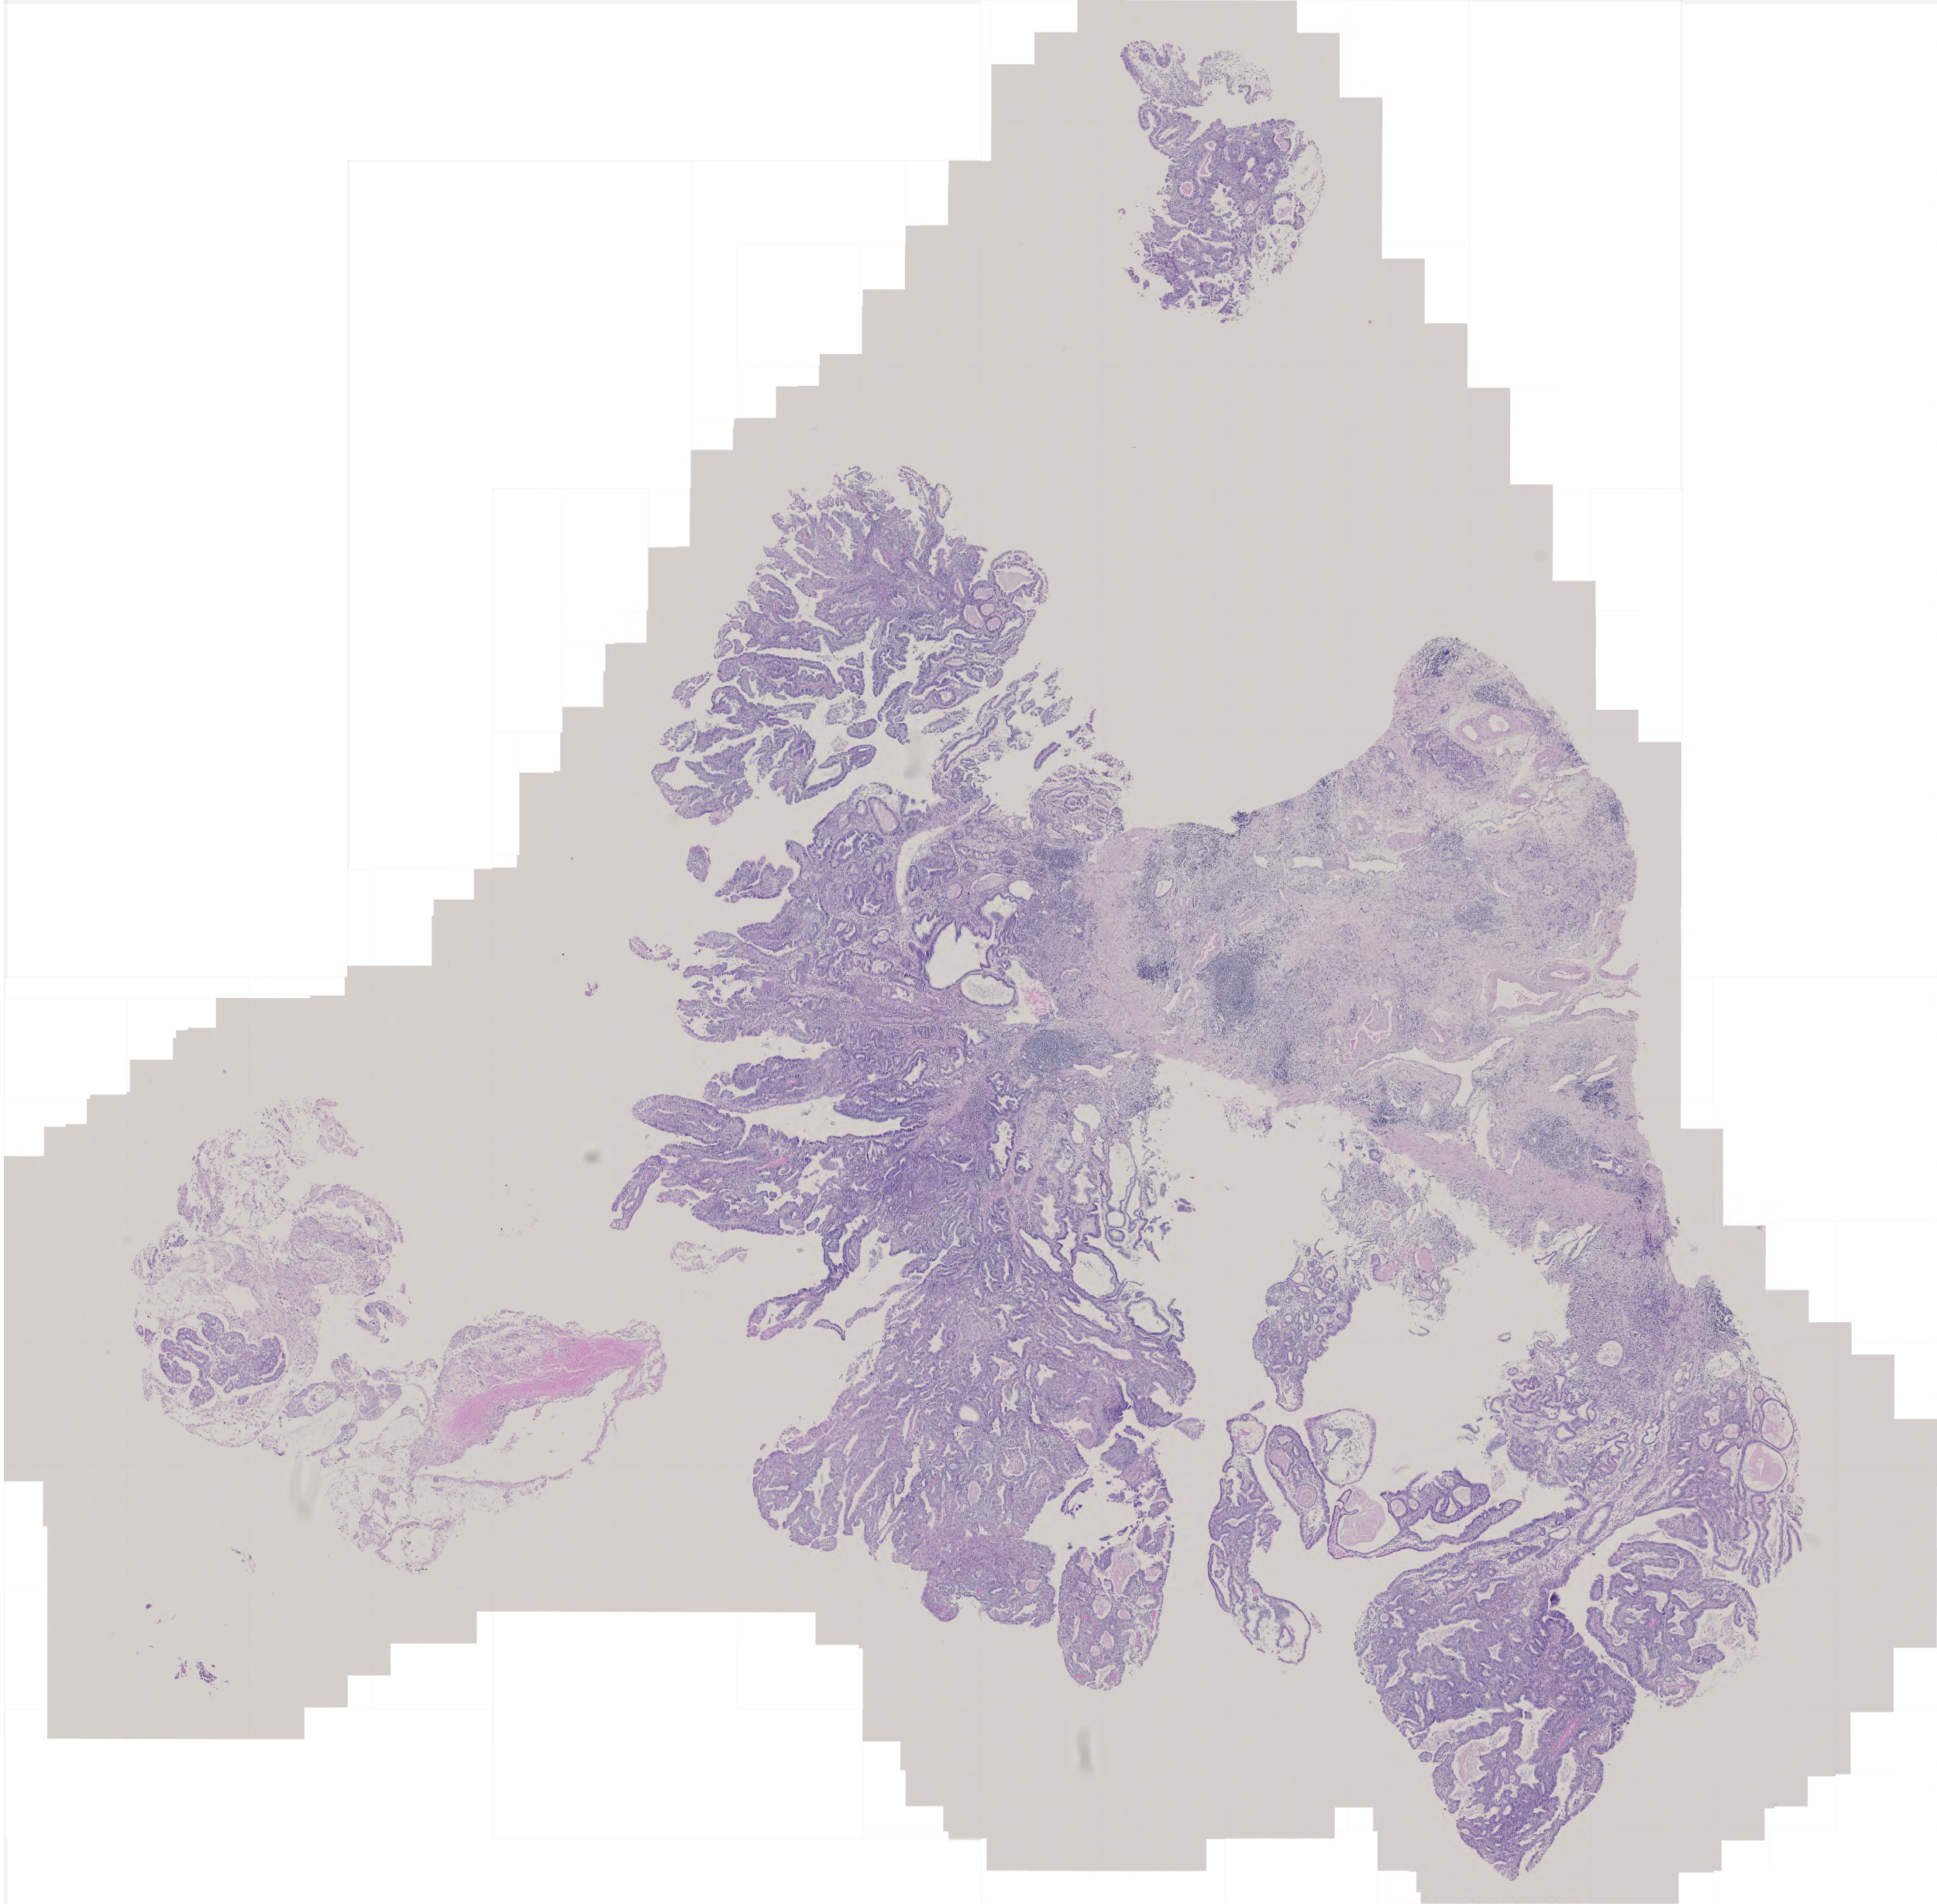
Digitized H&E tissue section (whole slide) — a low-resolution overview of the entire scanned area, about 5.0 x 4.9 mm; formalin-fixed paraffin-embedded (FFPE) diagnostic section; sample: primary tumour, stomach. Male patient; age at initial diagnosis 66 years. Histologic grade: G2 (moderately differentiated).
Lymph nodes positive (case pathology): 17 of 31 examined. TNM: T2 N3 M0. AJCC pathologic stage: IV (5th edition). Diagnosis: Adenocarcinoma, intestinal type (cardia, NOS).